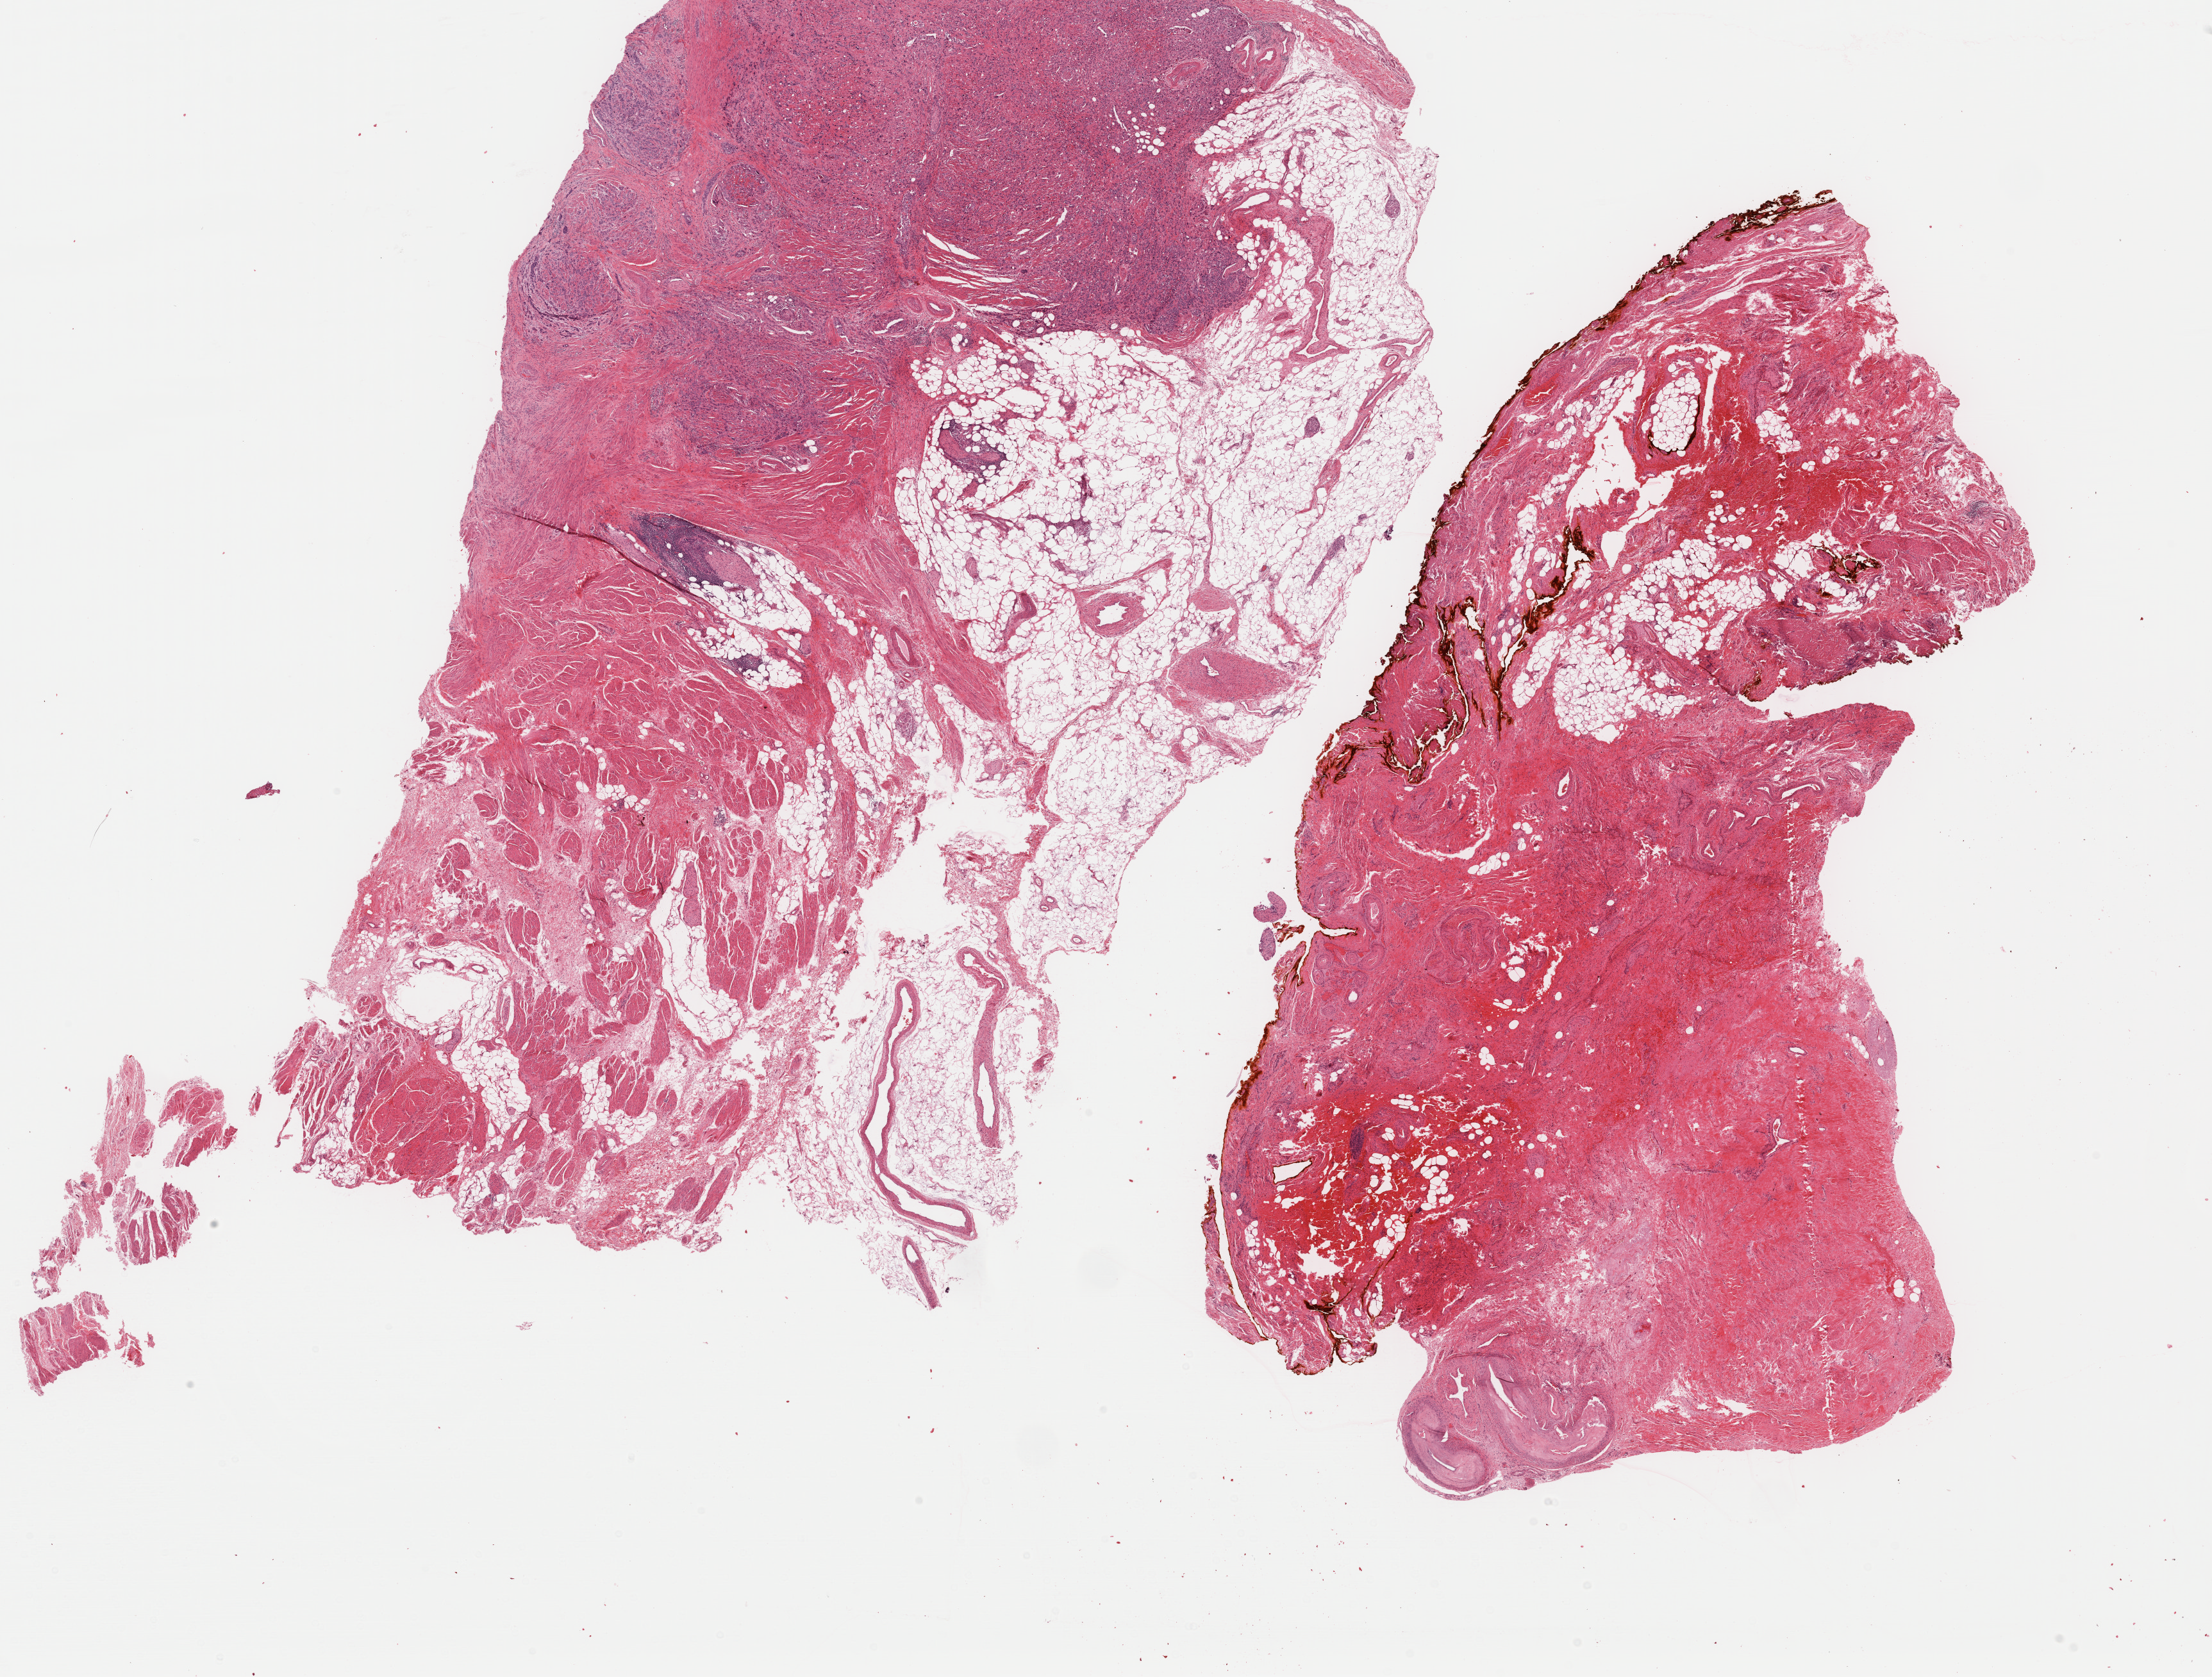
Digitized Hematoxylin and eosin (H&E) stained tissue section (whole slide), low-resolution overview of the scanned area, about 27.2 x 20.6 mm (slide scanned at 40x). FFPE section. Sample: primary tumour, bladder. Patient: female, age at initial diagnosis 78 years. Histologic grade: high grade.
Lymph nodes positive (case pathology): 1 of 16 examined. TNM: T3a N1 M0. Diagnosis: Transitional cell carcinoma (trigone of bladder). AJCC pathologic stage: IV.